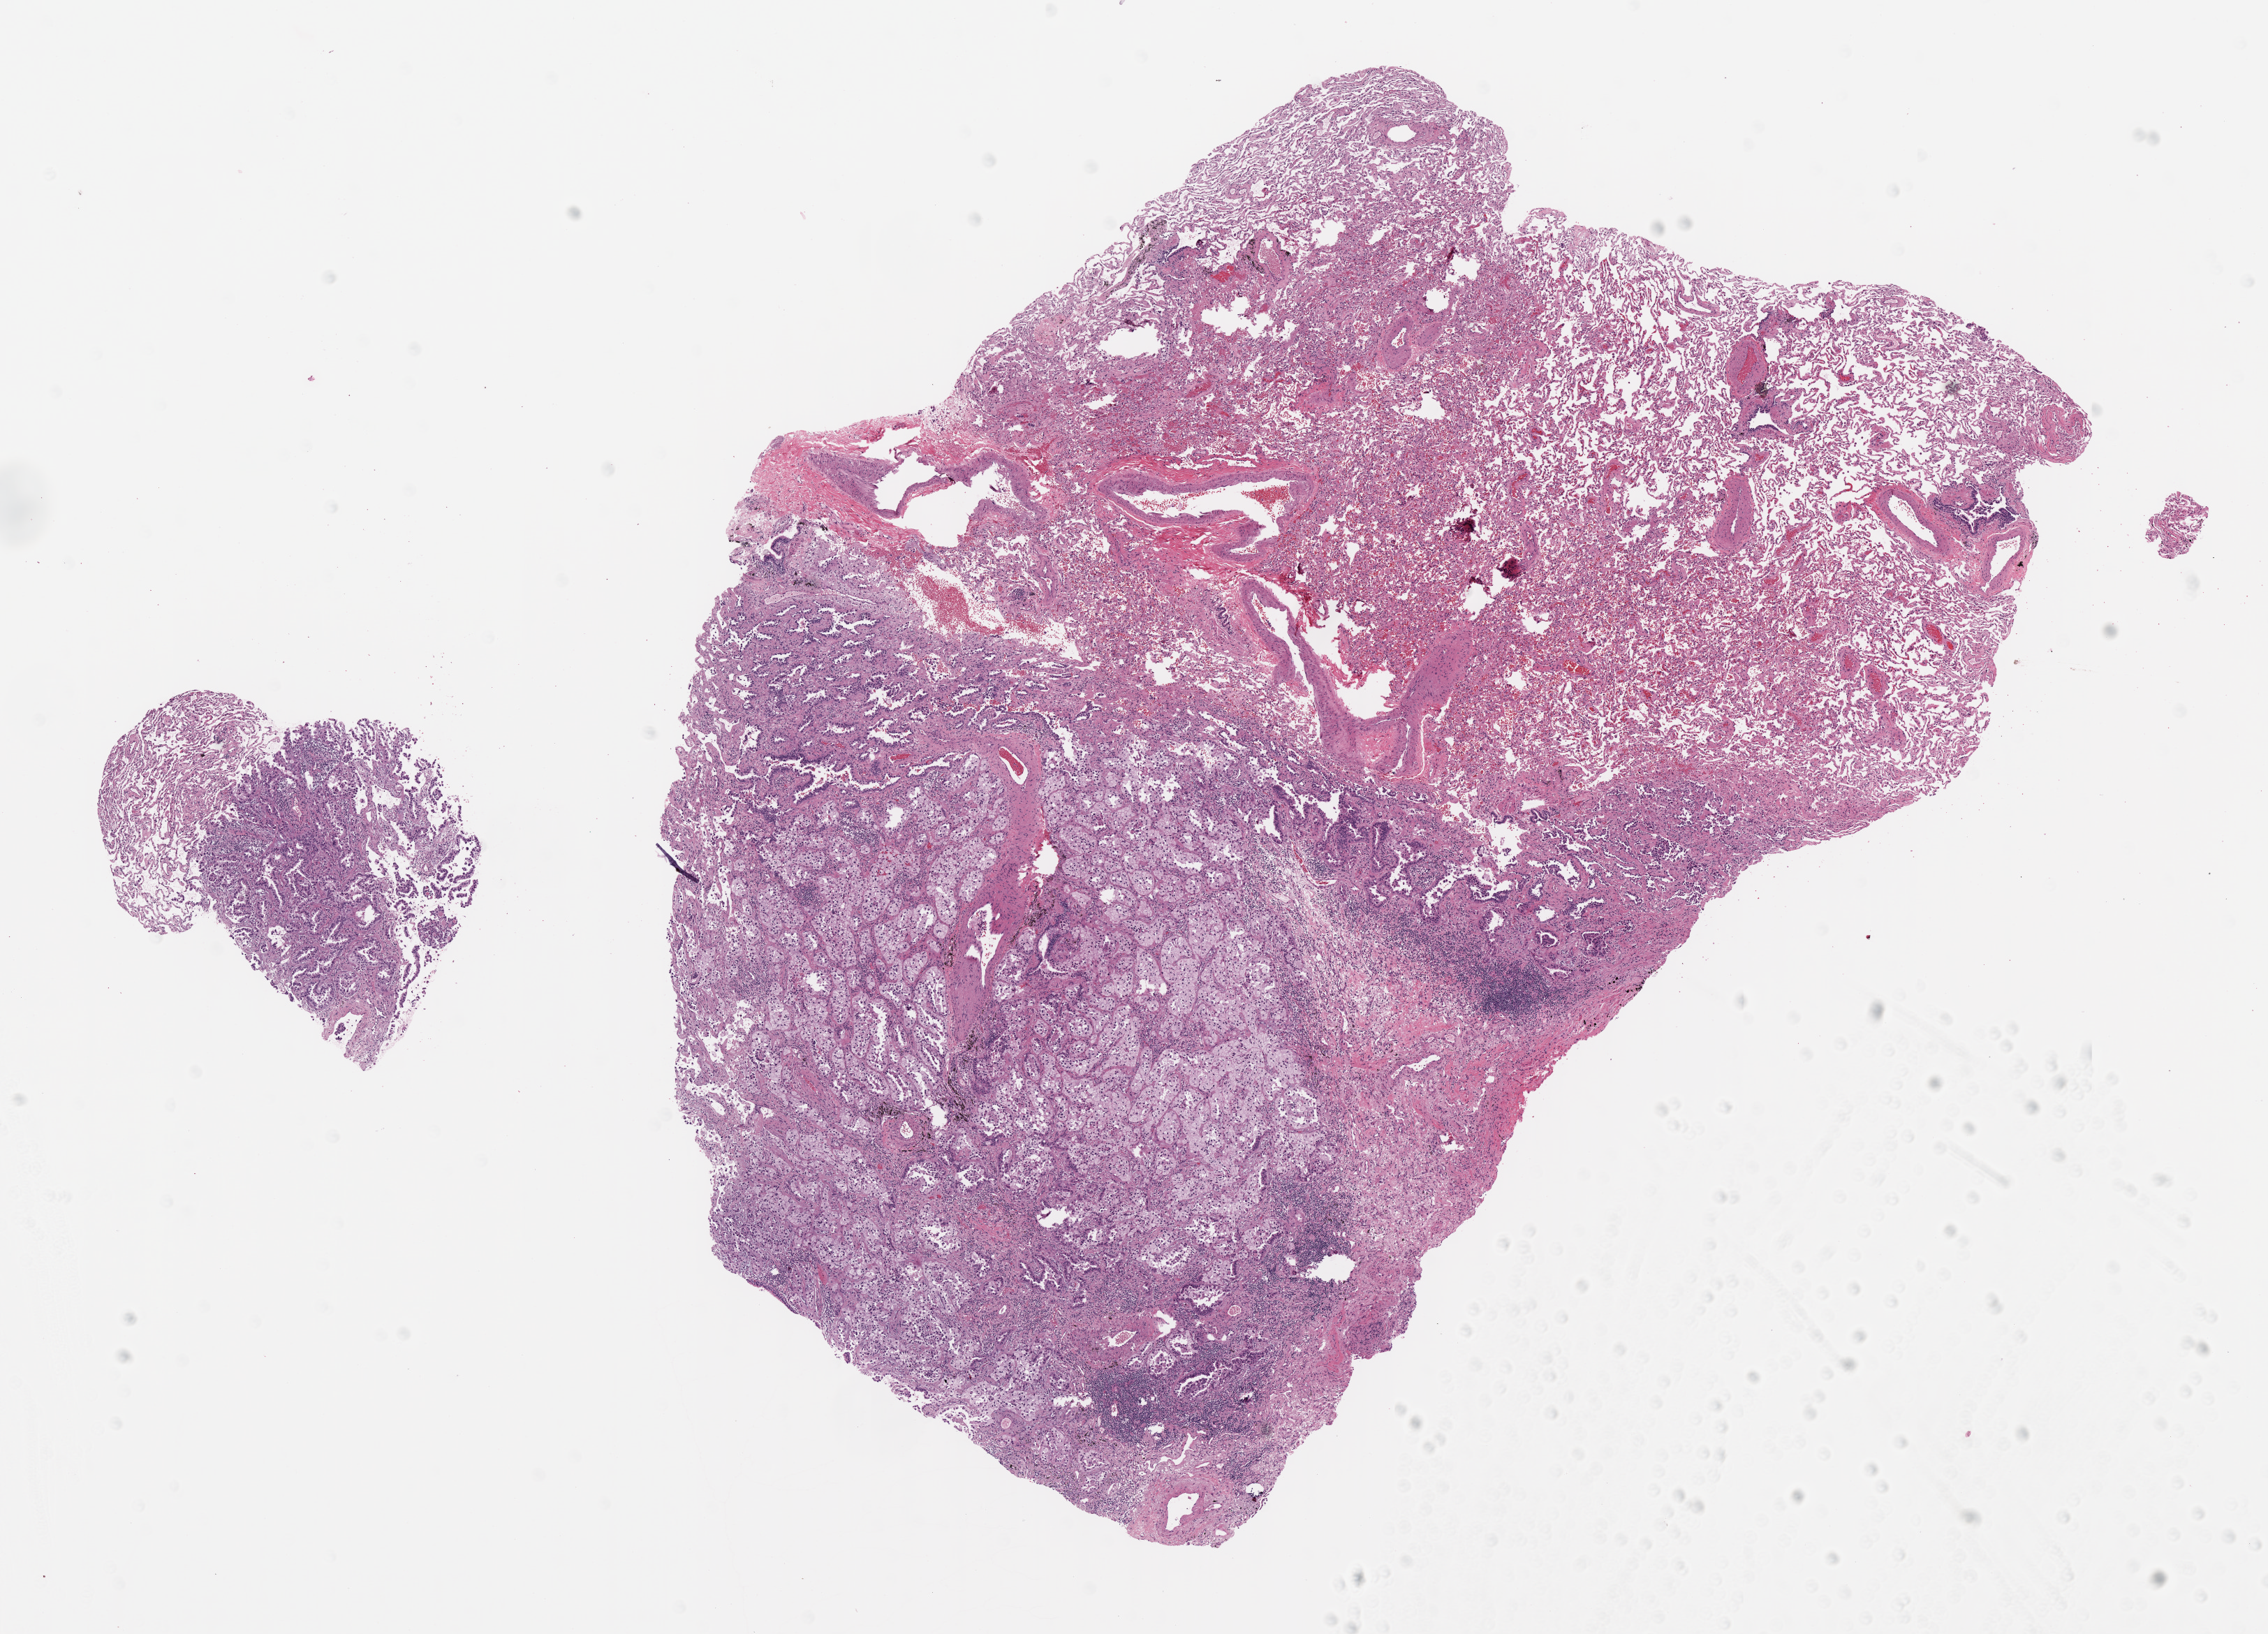
Digitized Hematoxylin and eosin (H&E) stained tissue section (whole slide), shown as a low-resolution overview of the whole scanned area (about 13.0 x 9.4 mm, slide scanned at 20x). Formalin-fixed paraffin-embedded (FFPE) diagnostic section. Lung, primary tumour sample. Patient sex: male.
* histologic diagnosis: Adenocarcinoma, NOS (upper lobe, lung)
* AJCC pathologic stage: IB
* laterality: left